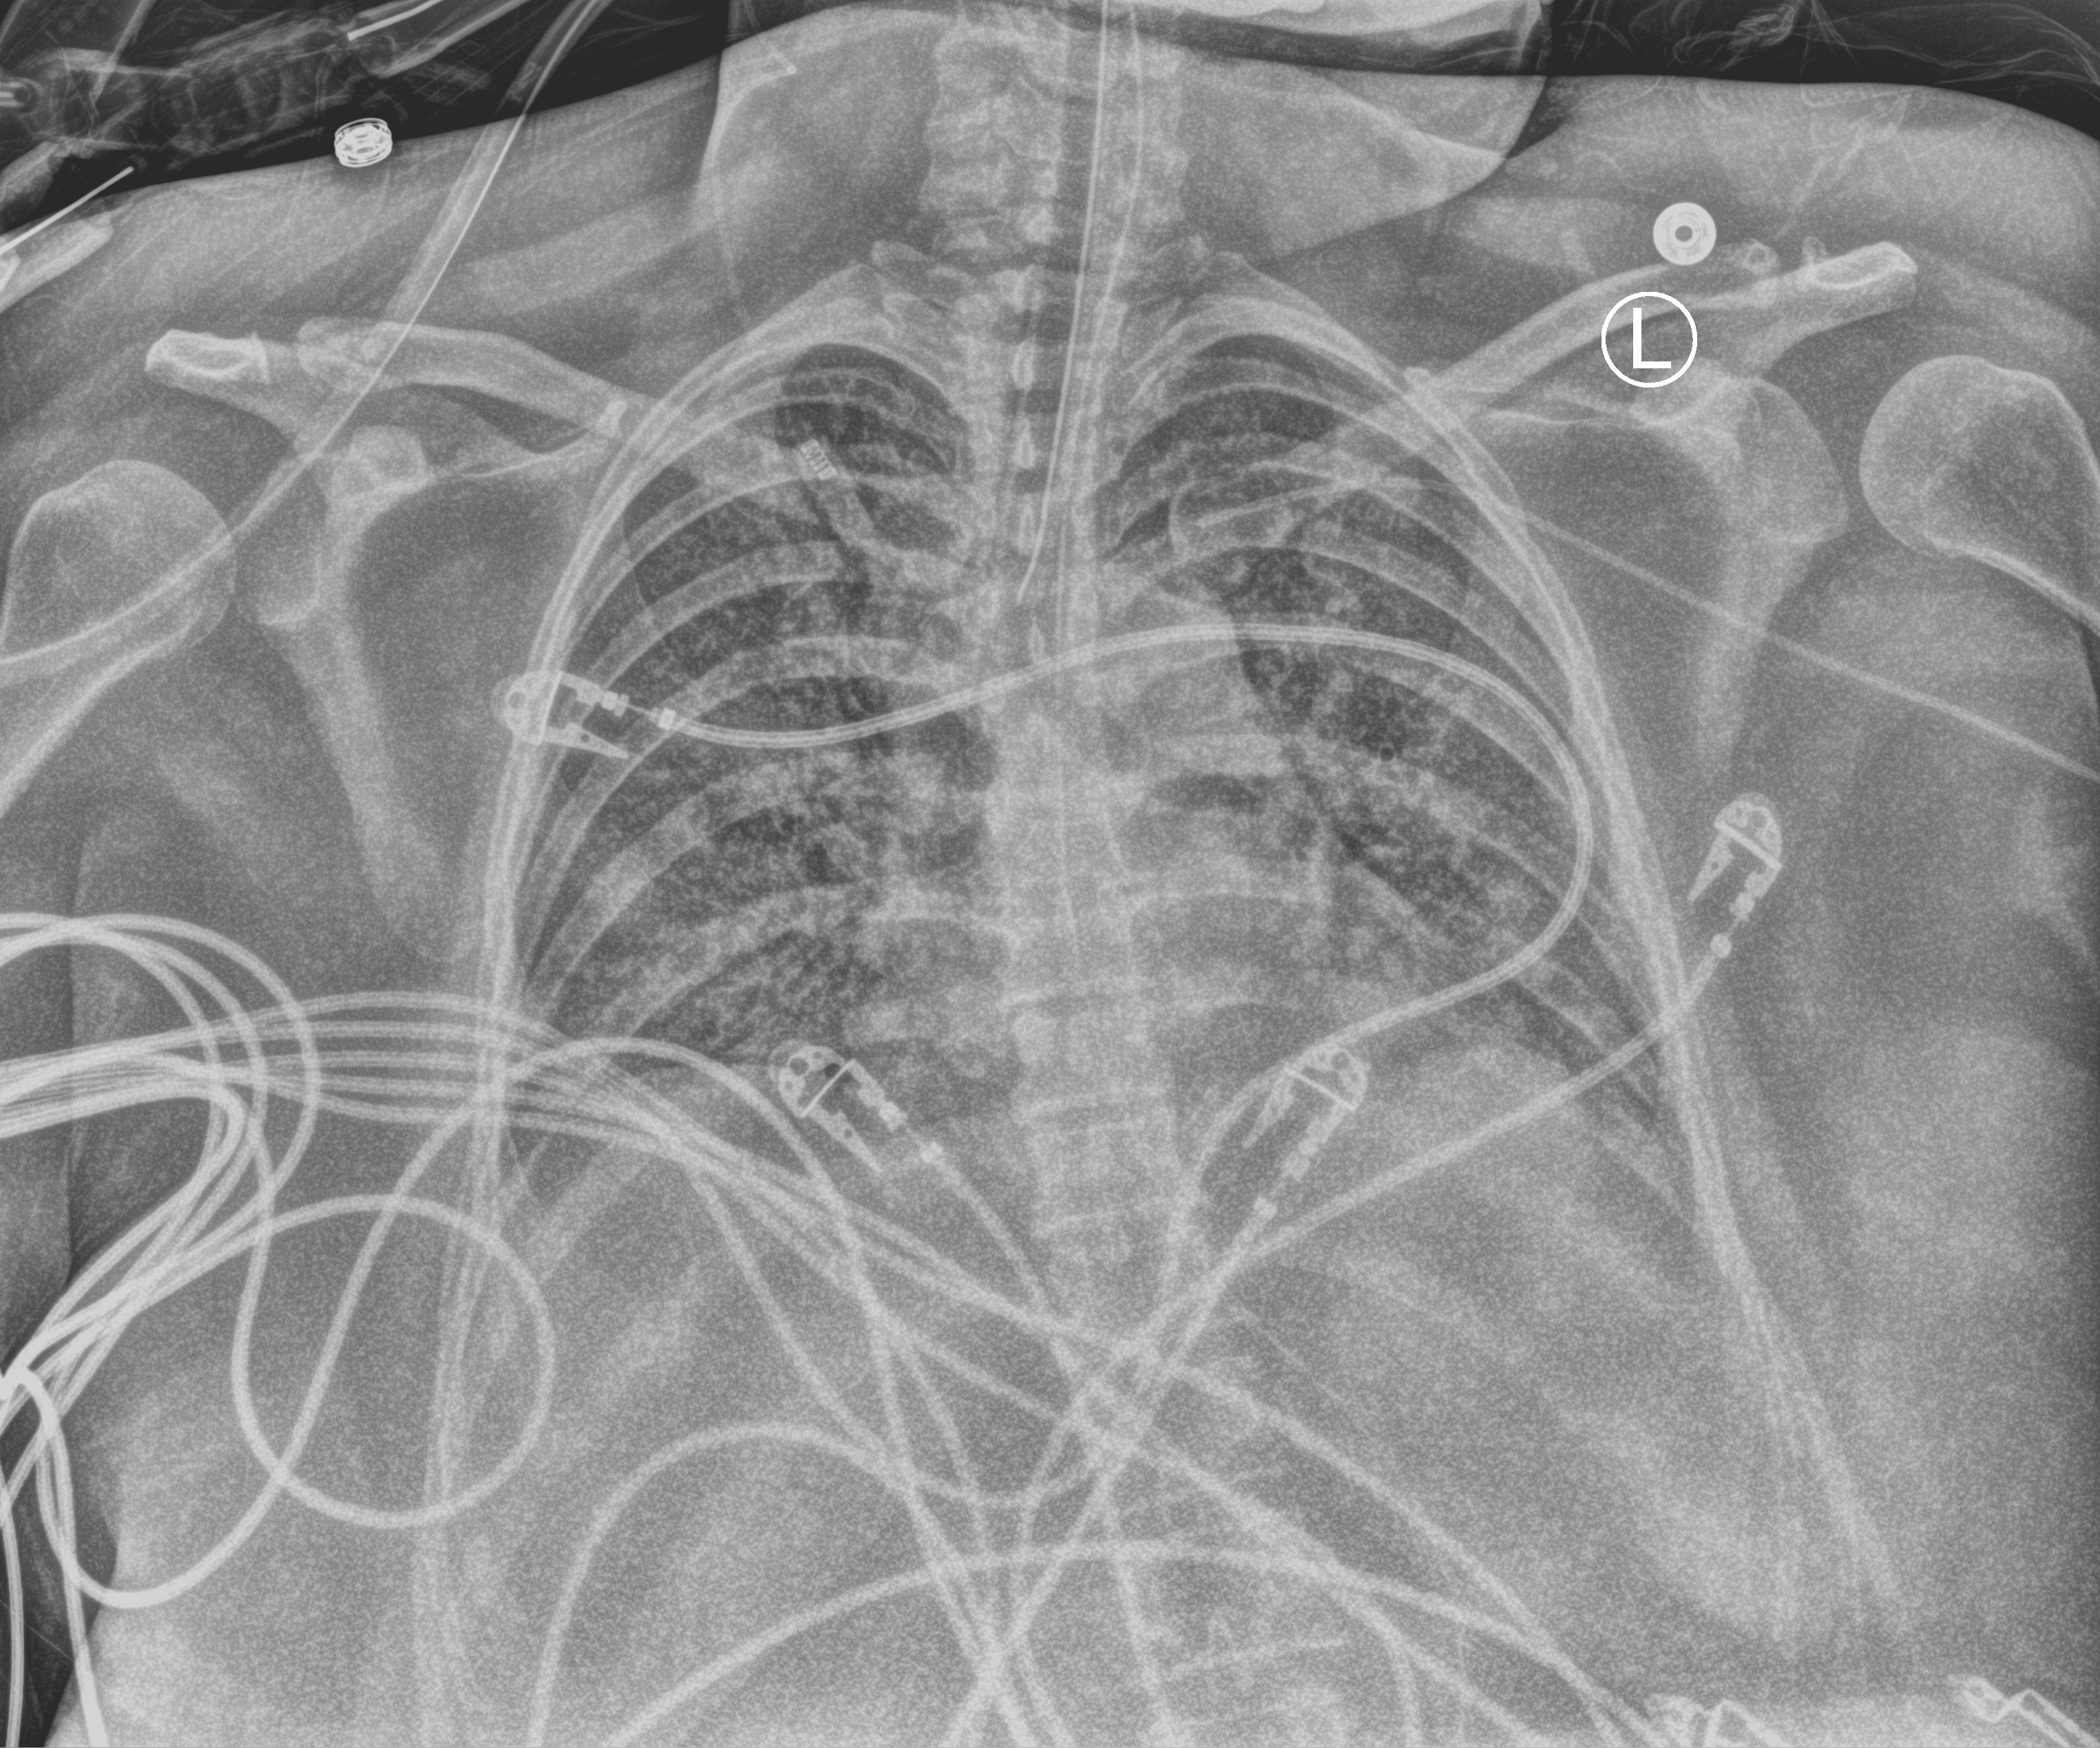
Portable chest radiograph, anteroposterior (AP) projection. Female patient hospitalised with COVID-19, age 18–59 years.
Admission-level facts for this patient (not findings on this image; timing relative to this image not recorded): mechanically ventilated during this hospital stay: yes; diabetes (admission record): no.